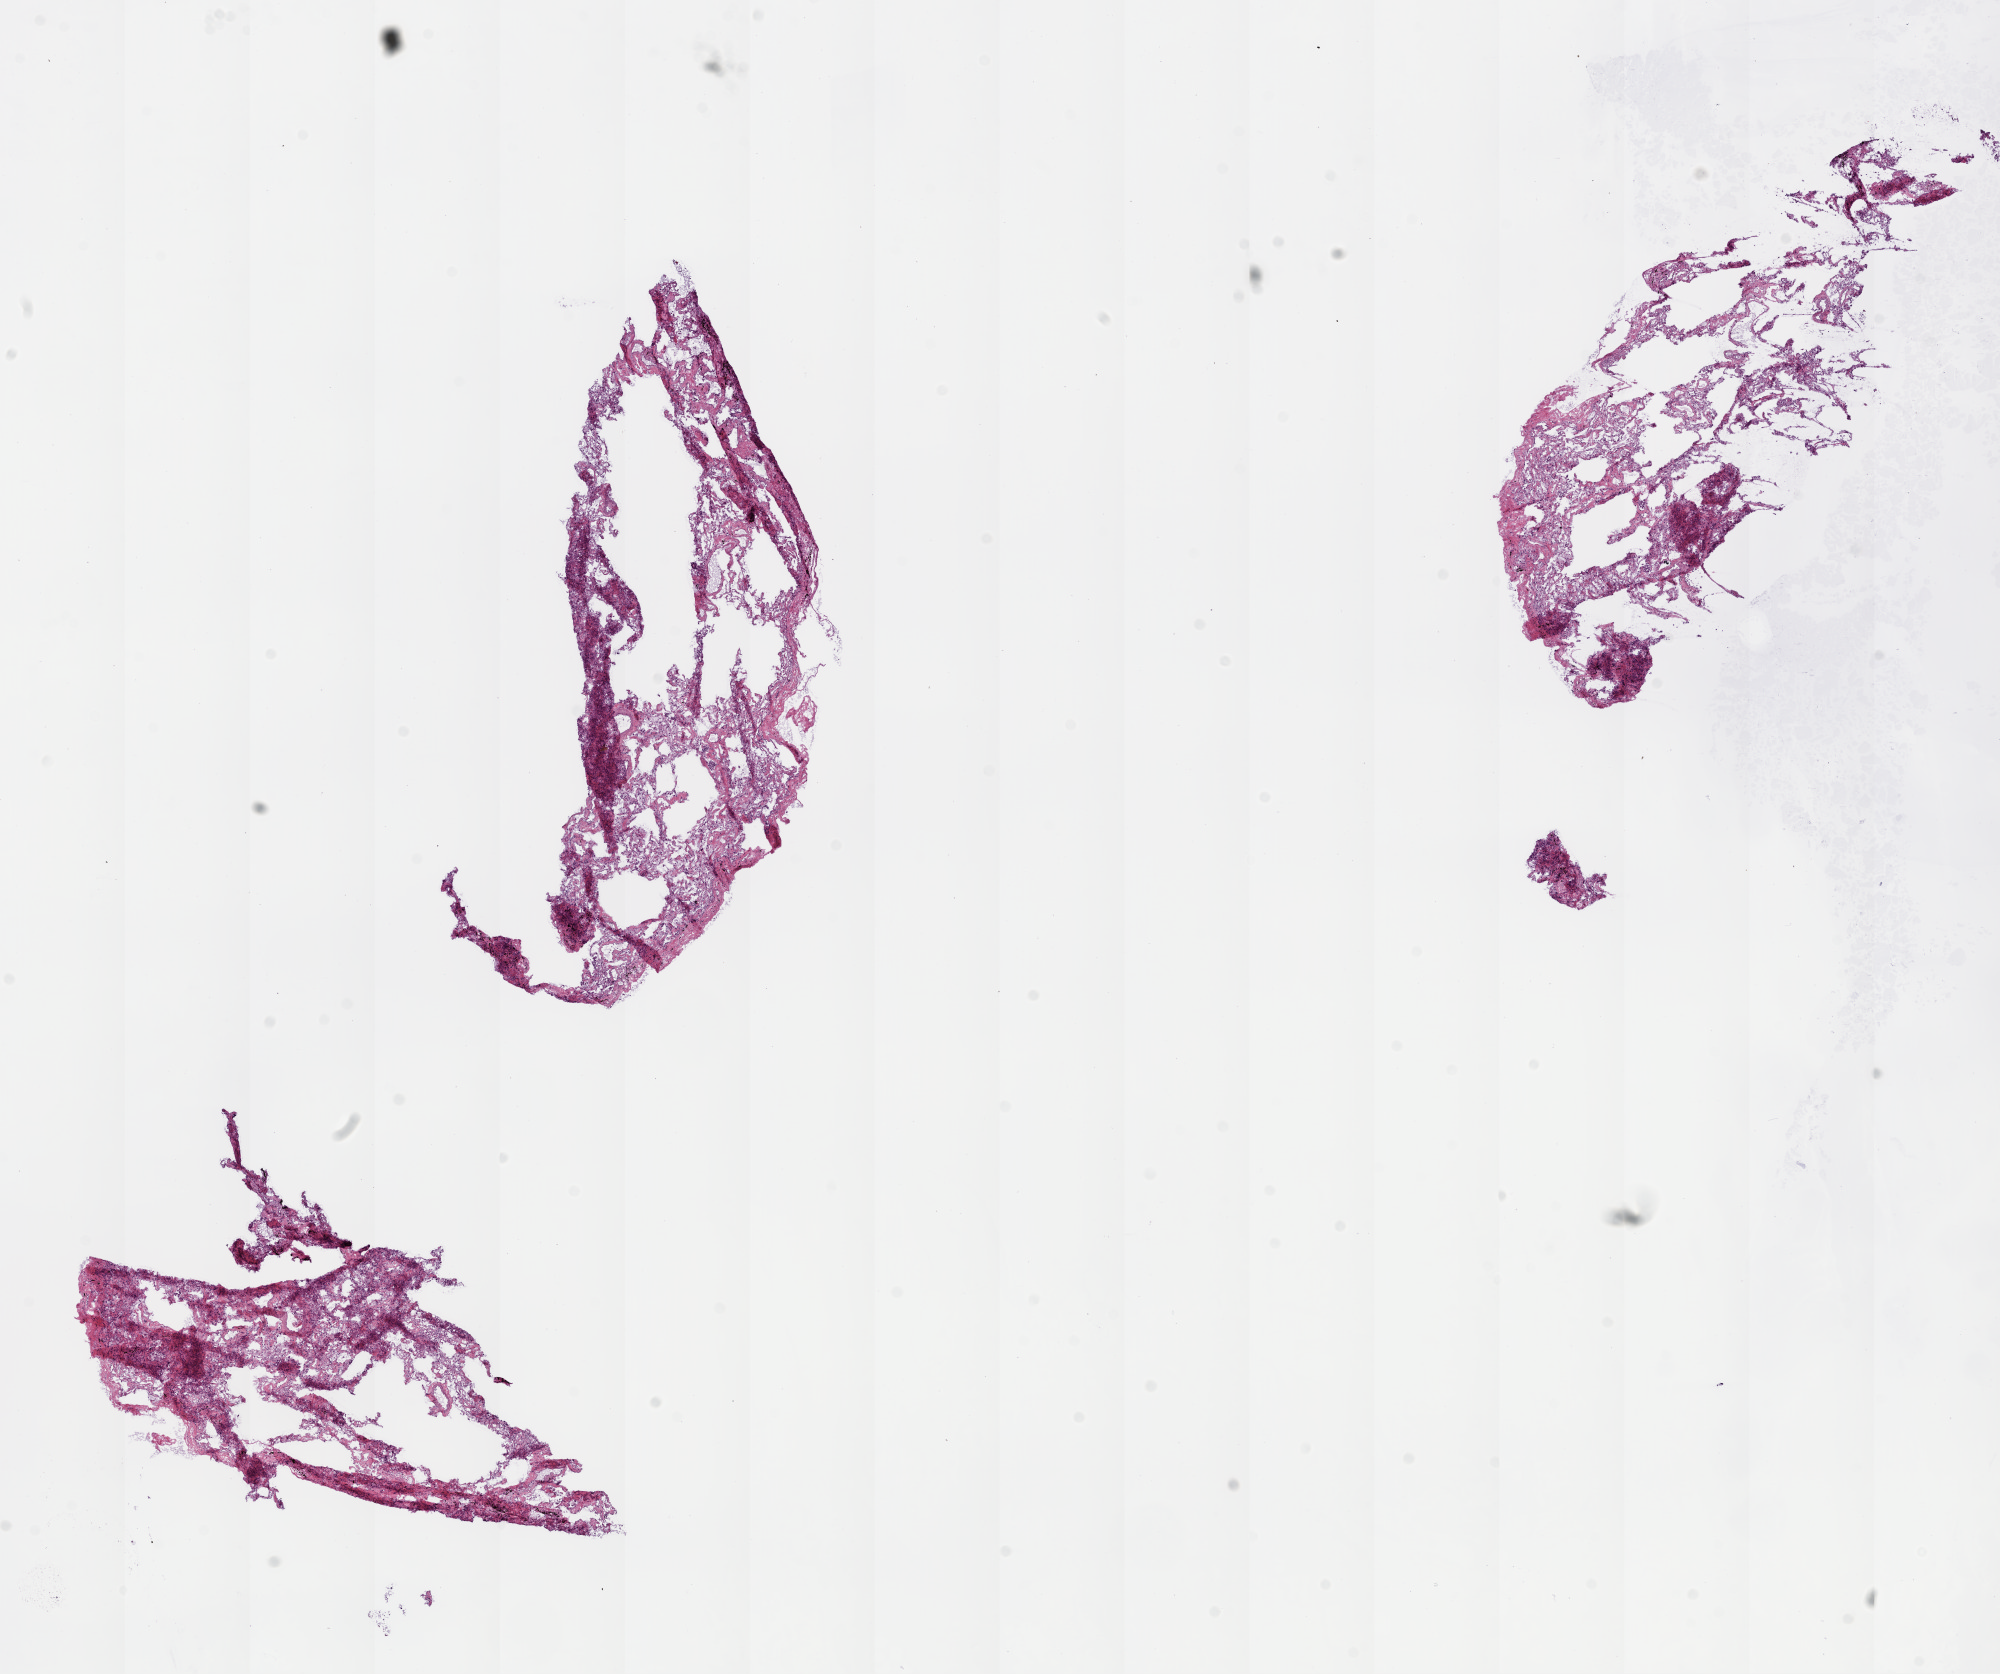
Hematoxylin and eosin (H&E) stained whole-slide image, low-resolution overview of the scanned area, about 16.0 x 13.4 mm, frozen section from the top of the tissue portion, lung, solid tissue normal (non-tumour tissue) sample. Patient: female, age at initial diagnosis 65 years.
This section: solid tissue normal sample (biorepository sample class). Patient diagnosis: Adenocarcinoma, NOS (lower lobe, lung).